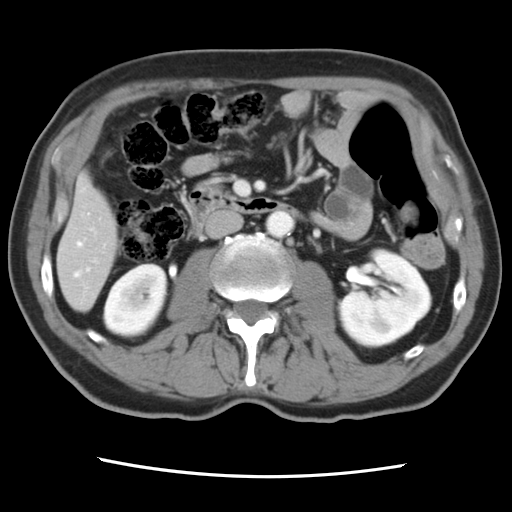
Contrast-enhanced abdominal CT, one axial slice; slice 26 of 83 in the series (ordered by position); intravenous contrast given; soft-tissue window (W 400 / L 40 HU); 512 × 512 image matrix, field of view 321 × 321 mm. Male patient, age 69 years. From the clinical record (not read from this slice): diagnosis: colorectal cancer liver metastases, imaged before liver resection; multiple liver metastases: yes; largest metastasis: 3.5 cm; disease in both lobes: no.
Annotated regions visible in this slice (expert manual segmentation):
- hepatic veins: bounding box <75,242,82,276> (left, top, right, bottom; pixels)
- liver: <59,178,117,311>
- planned liver remnant (the part of the liver to remain after resection): <59,178,118,310>
- portal vein (with intrahepatic branches): <87,268,90,271>